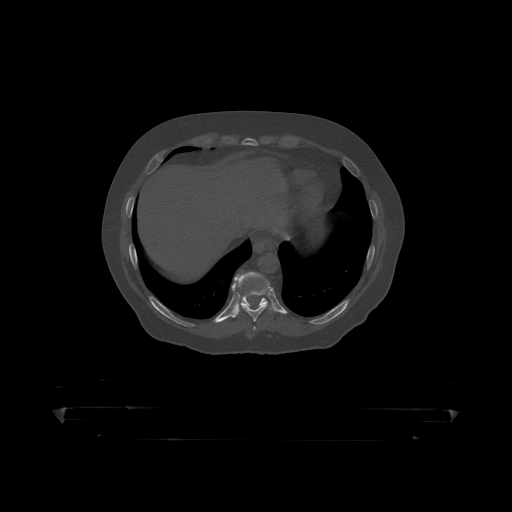
CT including the spine, one axial slice. Slice 229 of 390 in the series (ordered by position). Reconstruction kernel STANDARD. 120 kVp. Bone window (W 1800 / L 400 HU). 512 × 512 image matrix, field of view 650 × 650 mm. Patient: male, 60 years. Case-level facts recorded for this patient, not image findings: primary cancer: prostate.
Outlined on this slice (semi-automatically segmented with operator editing):
- T10 vertebra: bounding box (x1, y1, x2, y2) in pixels: (234, 273, 267, 307)
- T9 vertebra: (232, 280, 270, 319)